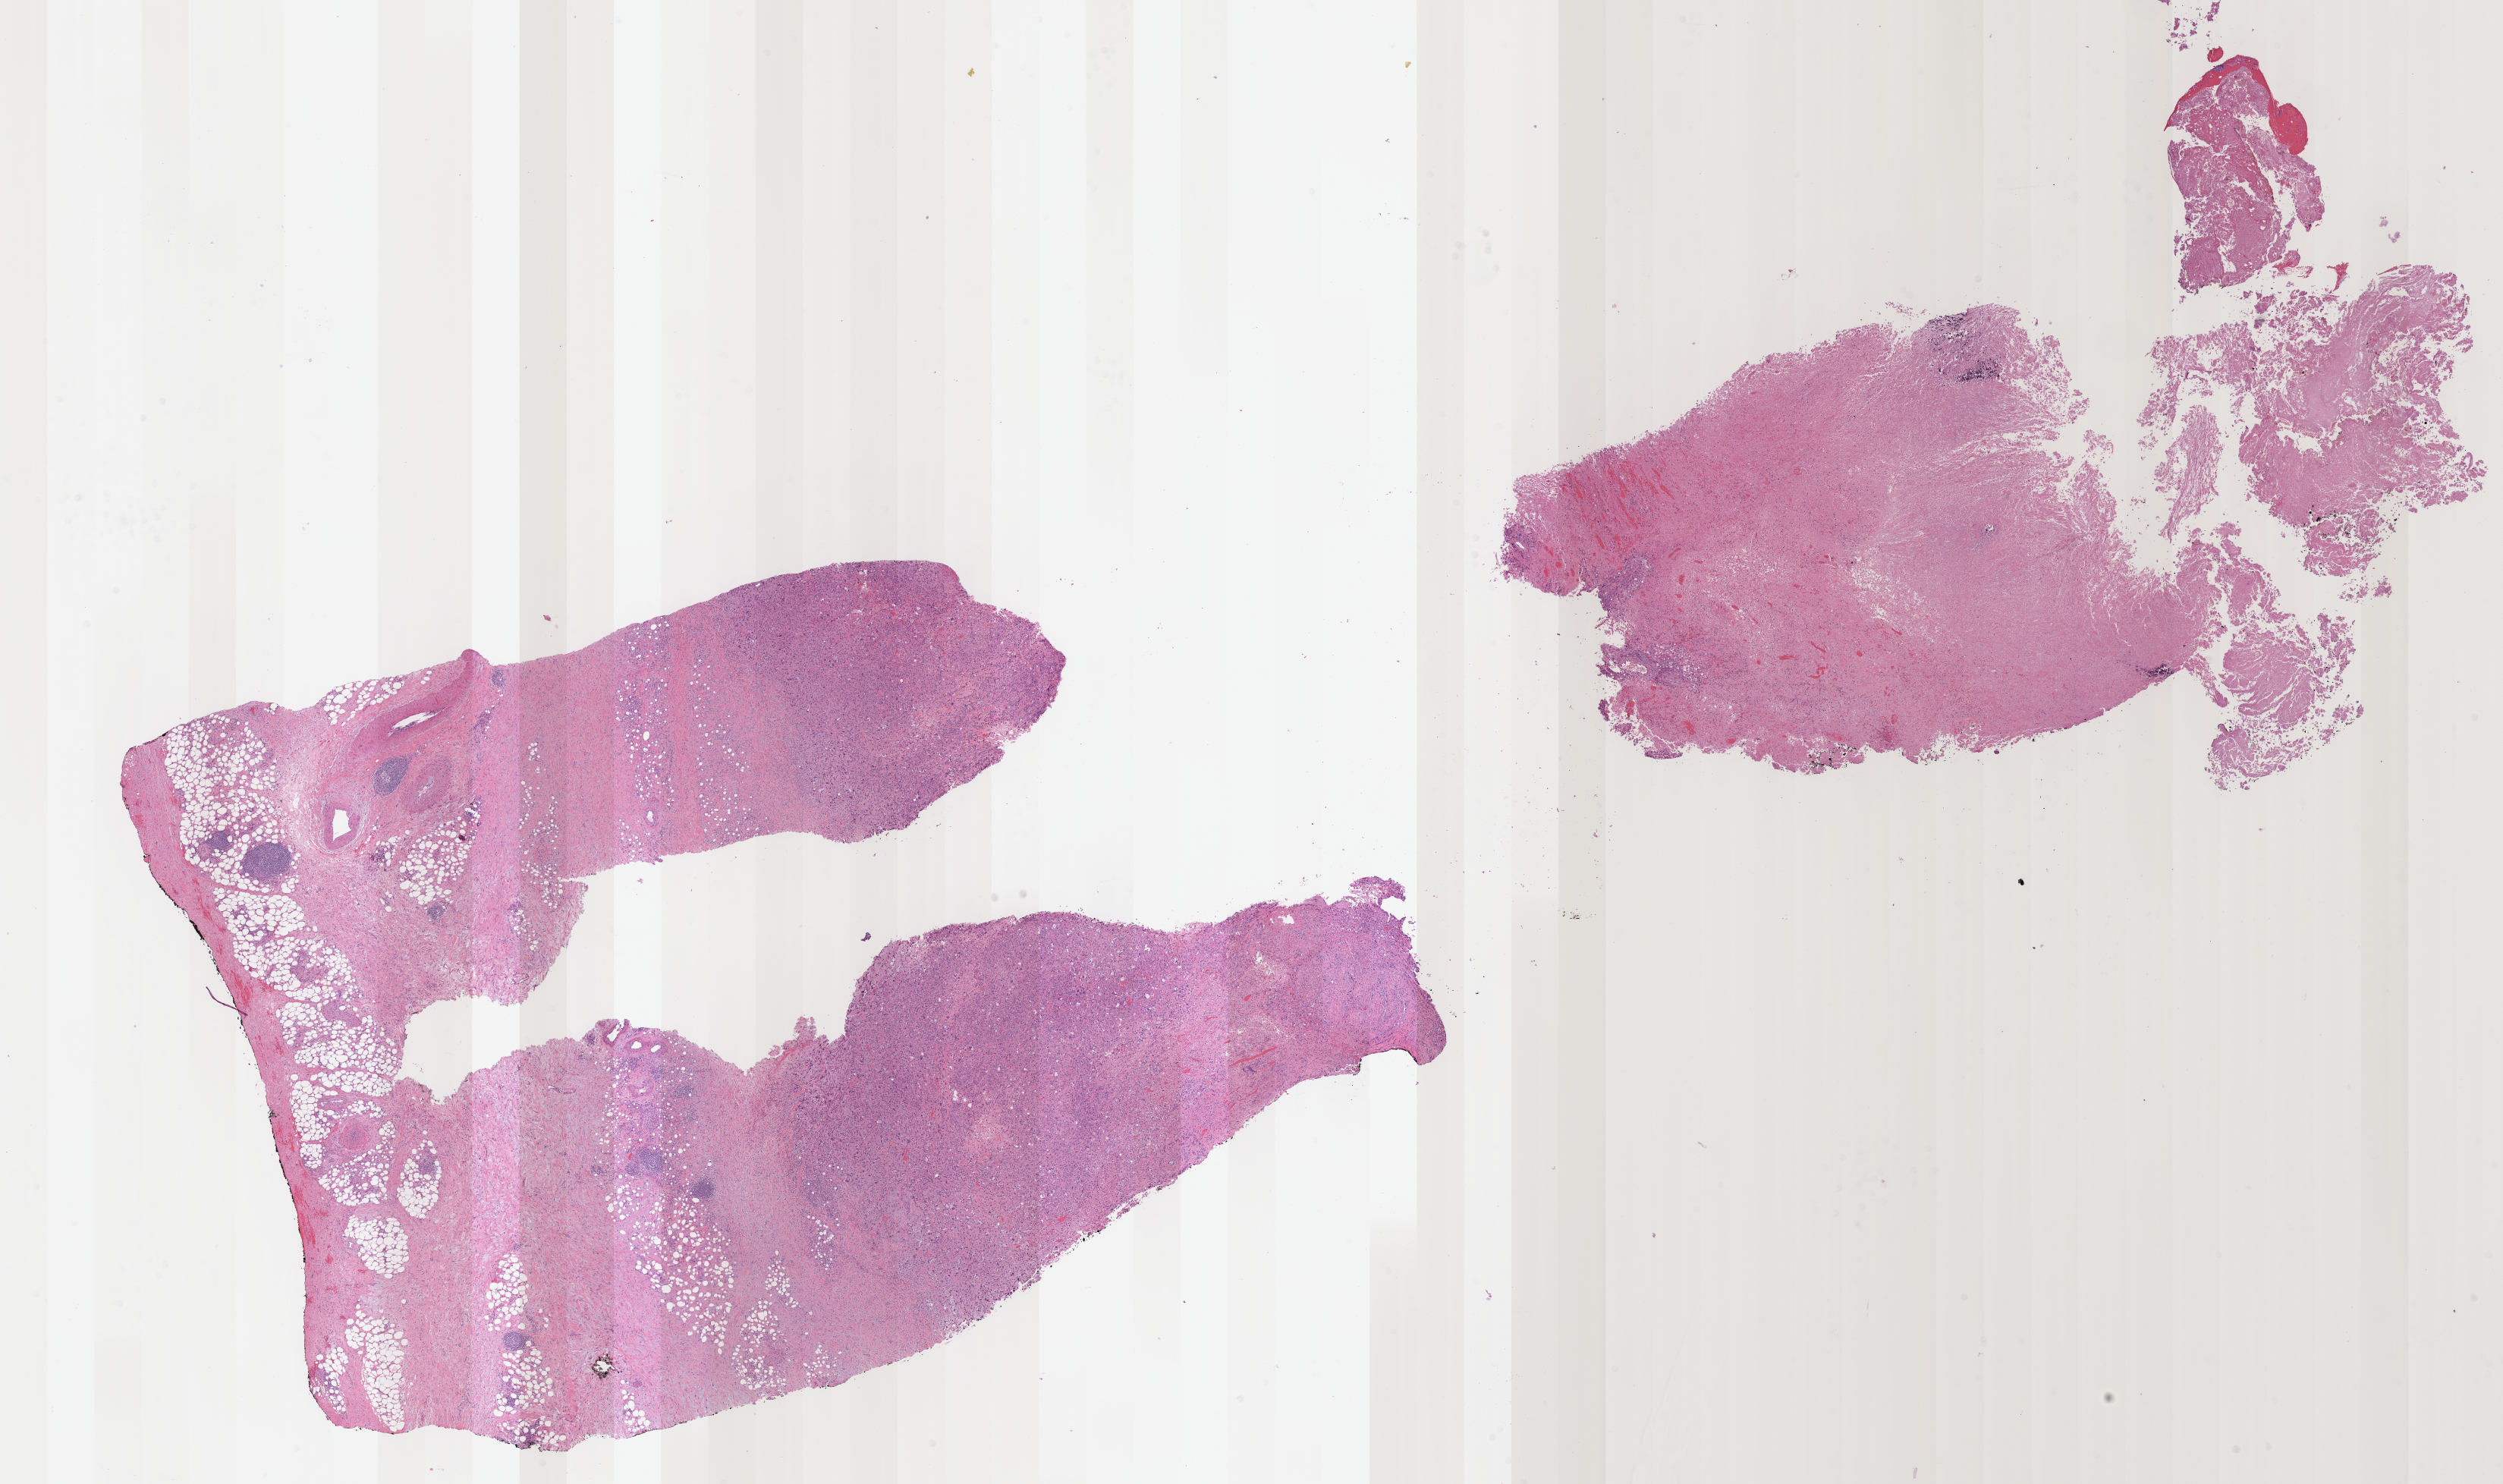
Whole-slide histology image, H&E-stained — whole scanned area (about 25.9 x 15.4 mm) shown as a low-resolution overview, formalin-fixed paraffin-embedded (FFPE) diagnostic section, primary tumour sample from the bladder. Male, age 59 years at initial diagnosis. Histologic grade: high grade.
- pathologic diagnosis: Transitional cell carcinoma
- lymph nodes positive (case pathology): 0 of 9 examined
- TNM: T2b N0 M0
- AJCC pathologic stage: II